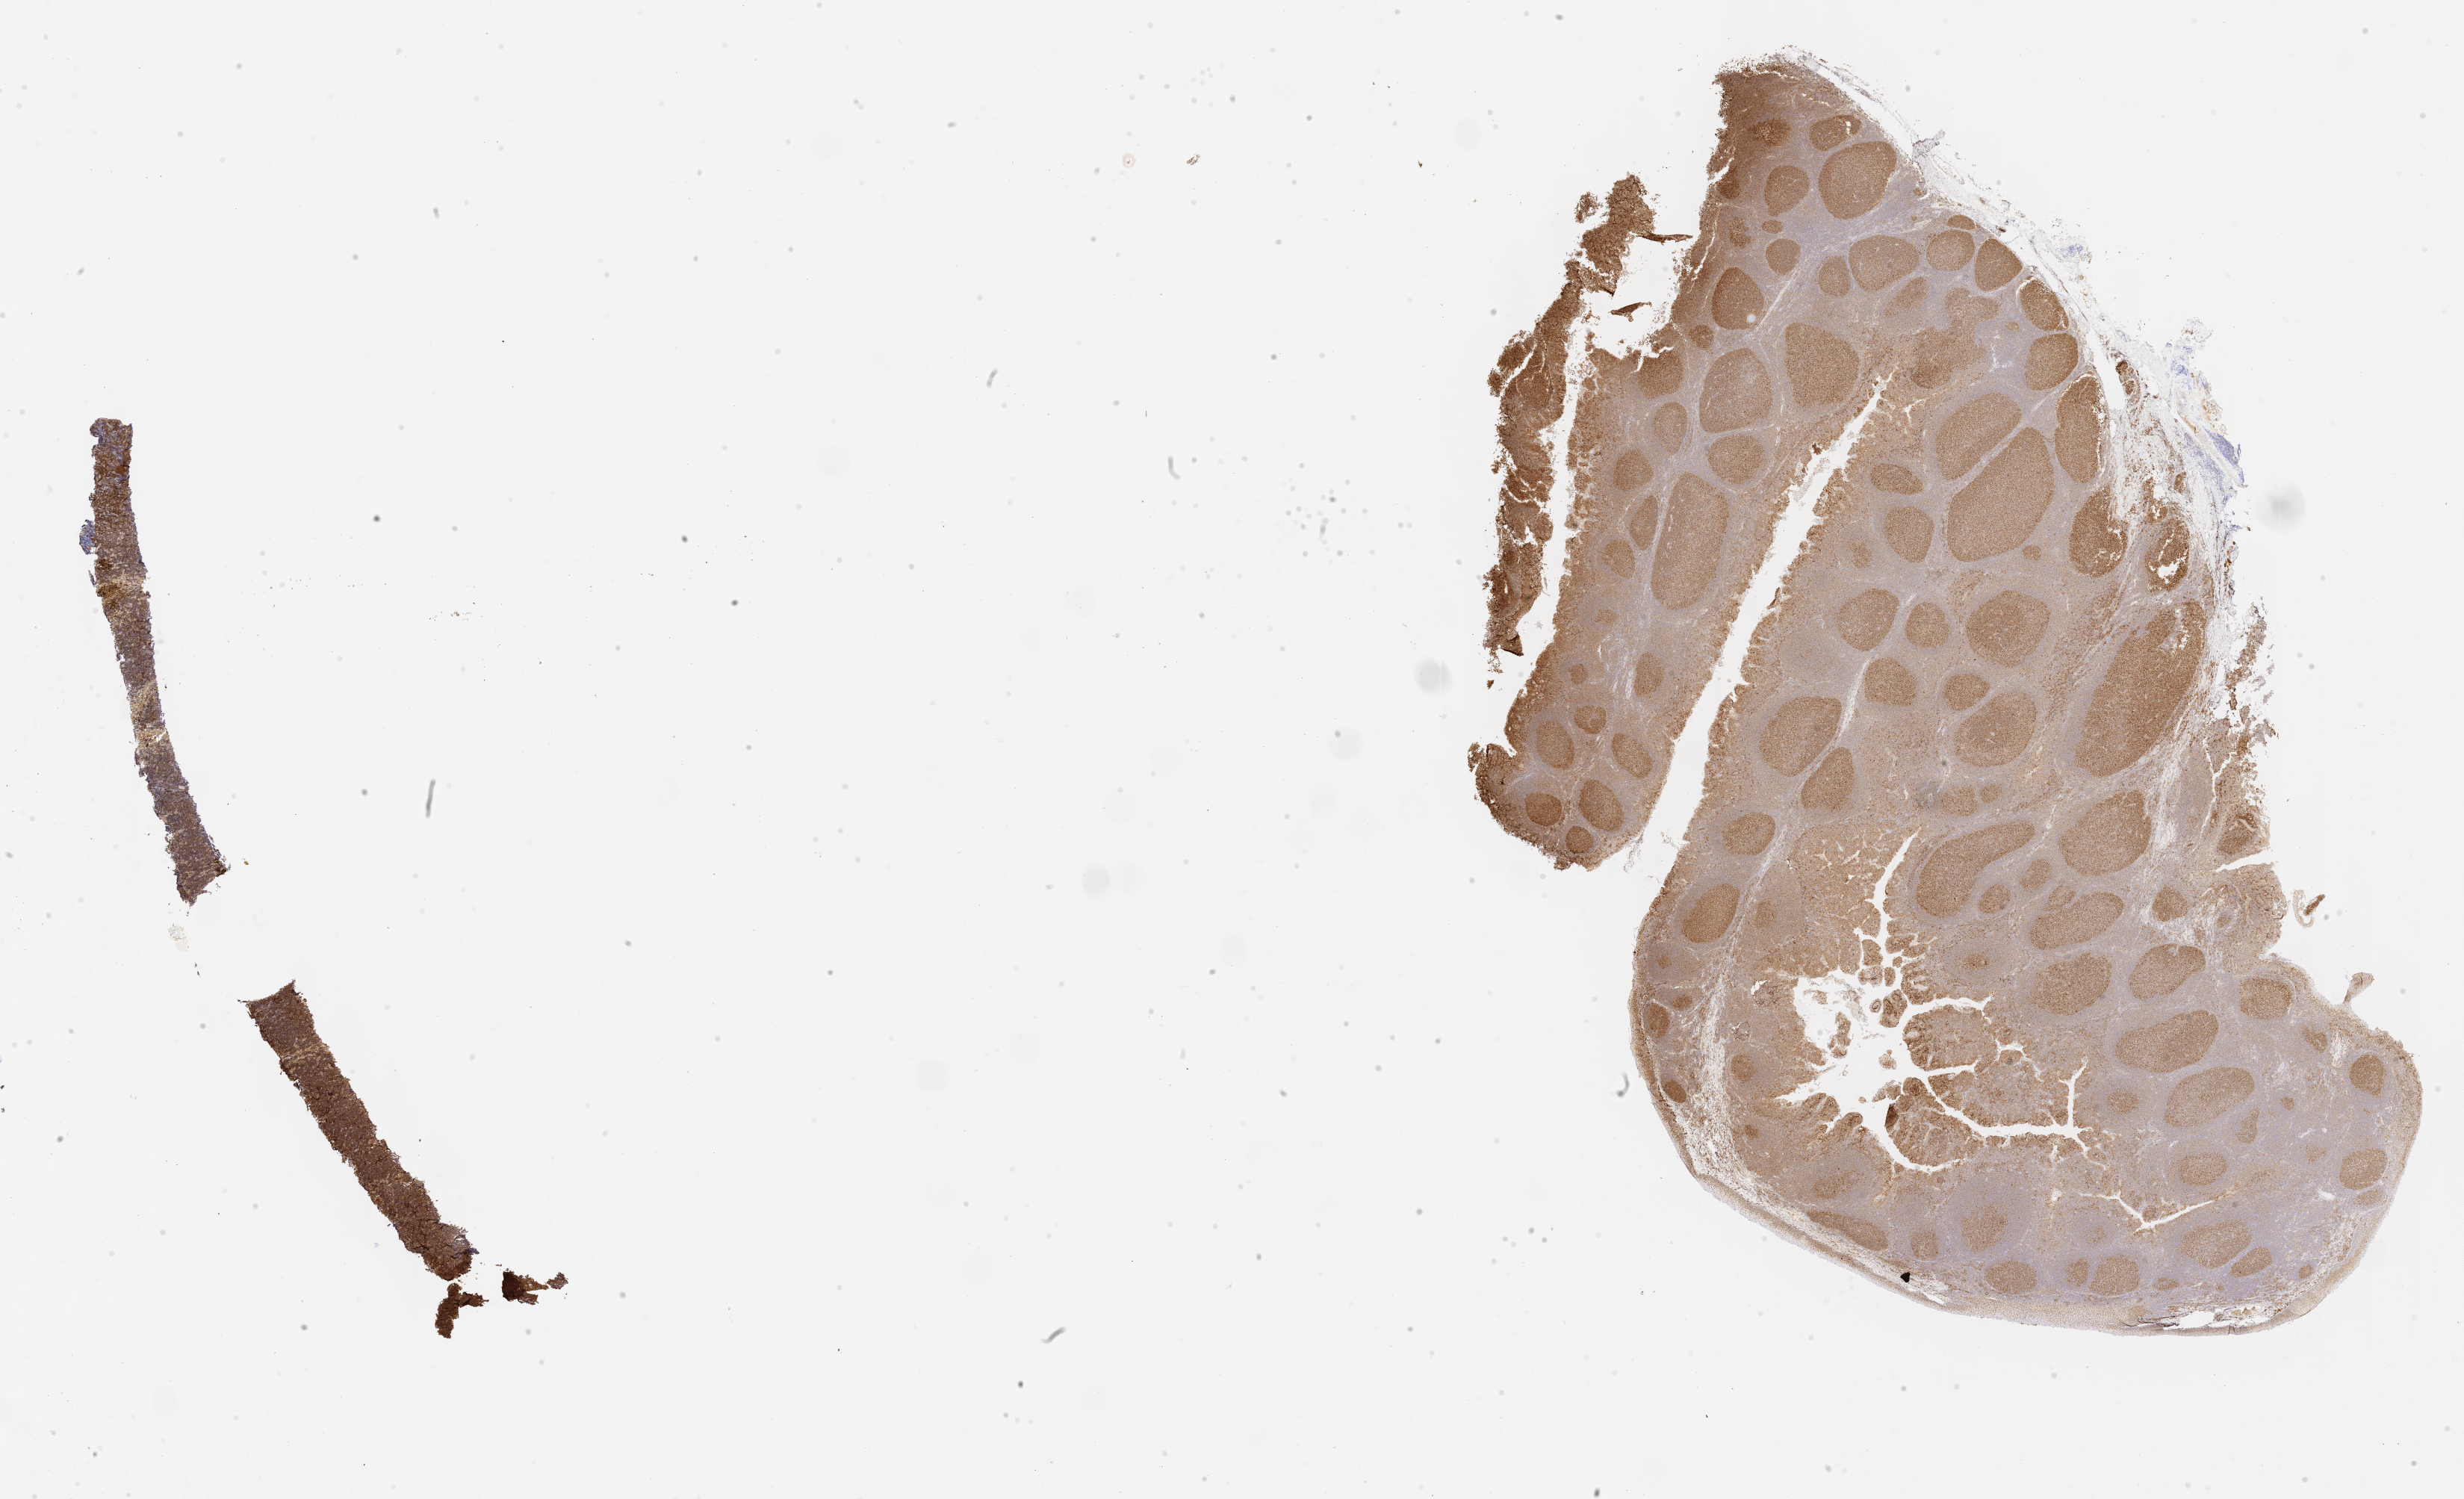
Whole-slide image, immunohistochemical stain for BCL6 — low-resolution overview of the scanned area, about 26.7 x 16.2 mm. Female patient.
- specimen: tumor tissue